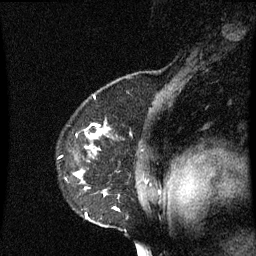
Breast MRI (dynamic contrast-enhanced), one sagittal slice. Slice 51 of 60 in the series (ordered by position). Dynamic contrast-enhanced series, image 2 of 3 at this slice position (ordered by acquisition). 1.5 T. TE 4.2 ms, TR 8.9 ms. 256 × 256 image matrix, field of view 200 × 200 mm. Female patient, age 53 years. Case-level facts recorded for this patient, not image findings: setting: breast cancer imaged before/during neoadjuvant chemotherapy; receptor status: HR-positive, HER2-negative.
Outlined on this slice (semi-automatically segmented with operator editing):
- analysis volume of interest (the breast-tissue region the enhancement analysis was run in; not a lesion): bounding box (x1, y1, x2, y2) in pixels: (66, 130, 157, 227)
- tumour enhancement mask (voxels above the 70 % enhancement threshold inside the analysis volume of interest): (76, 130, 119, 219)